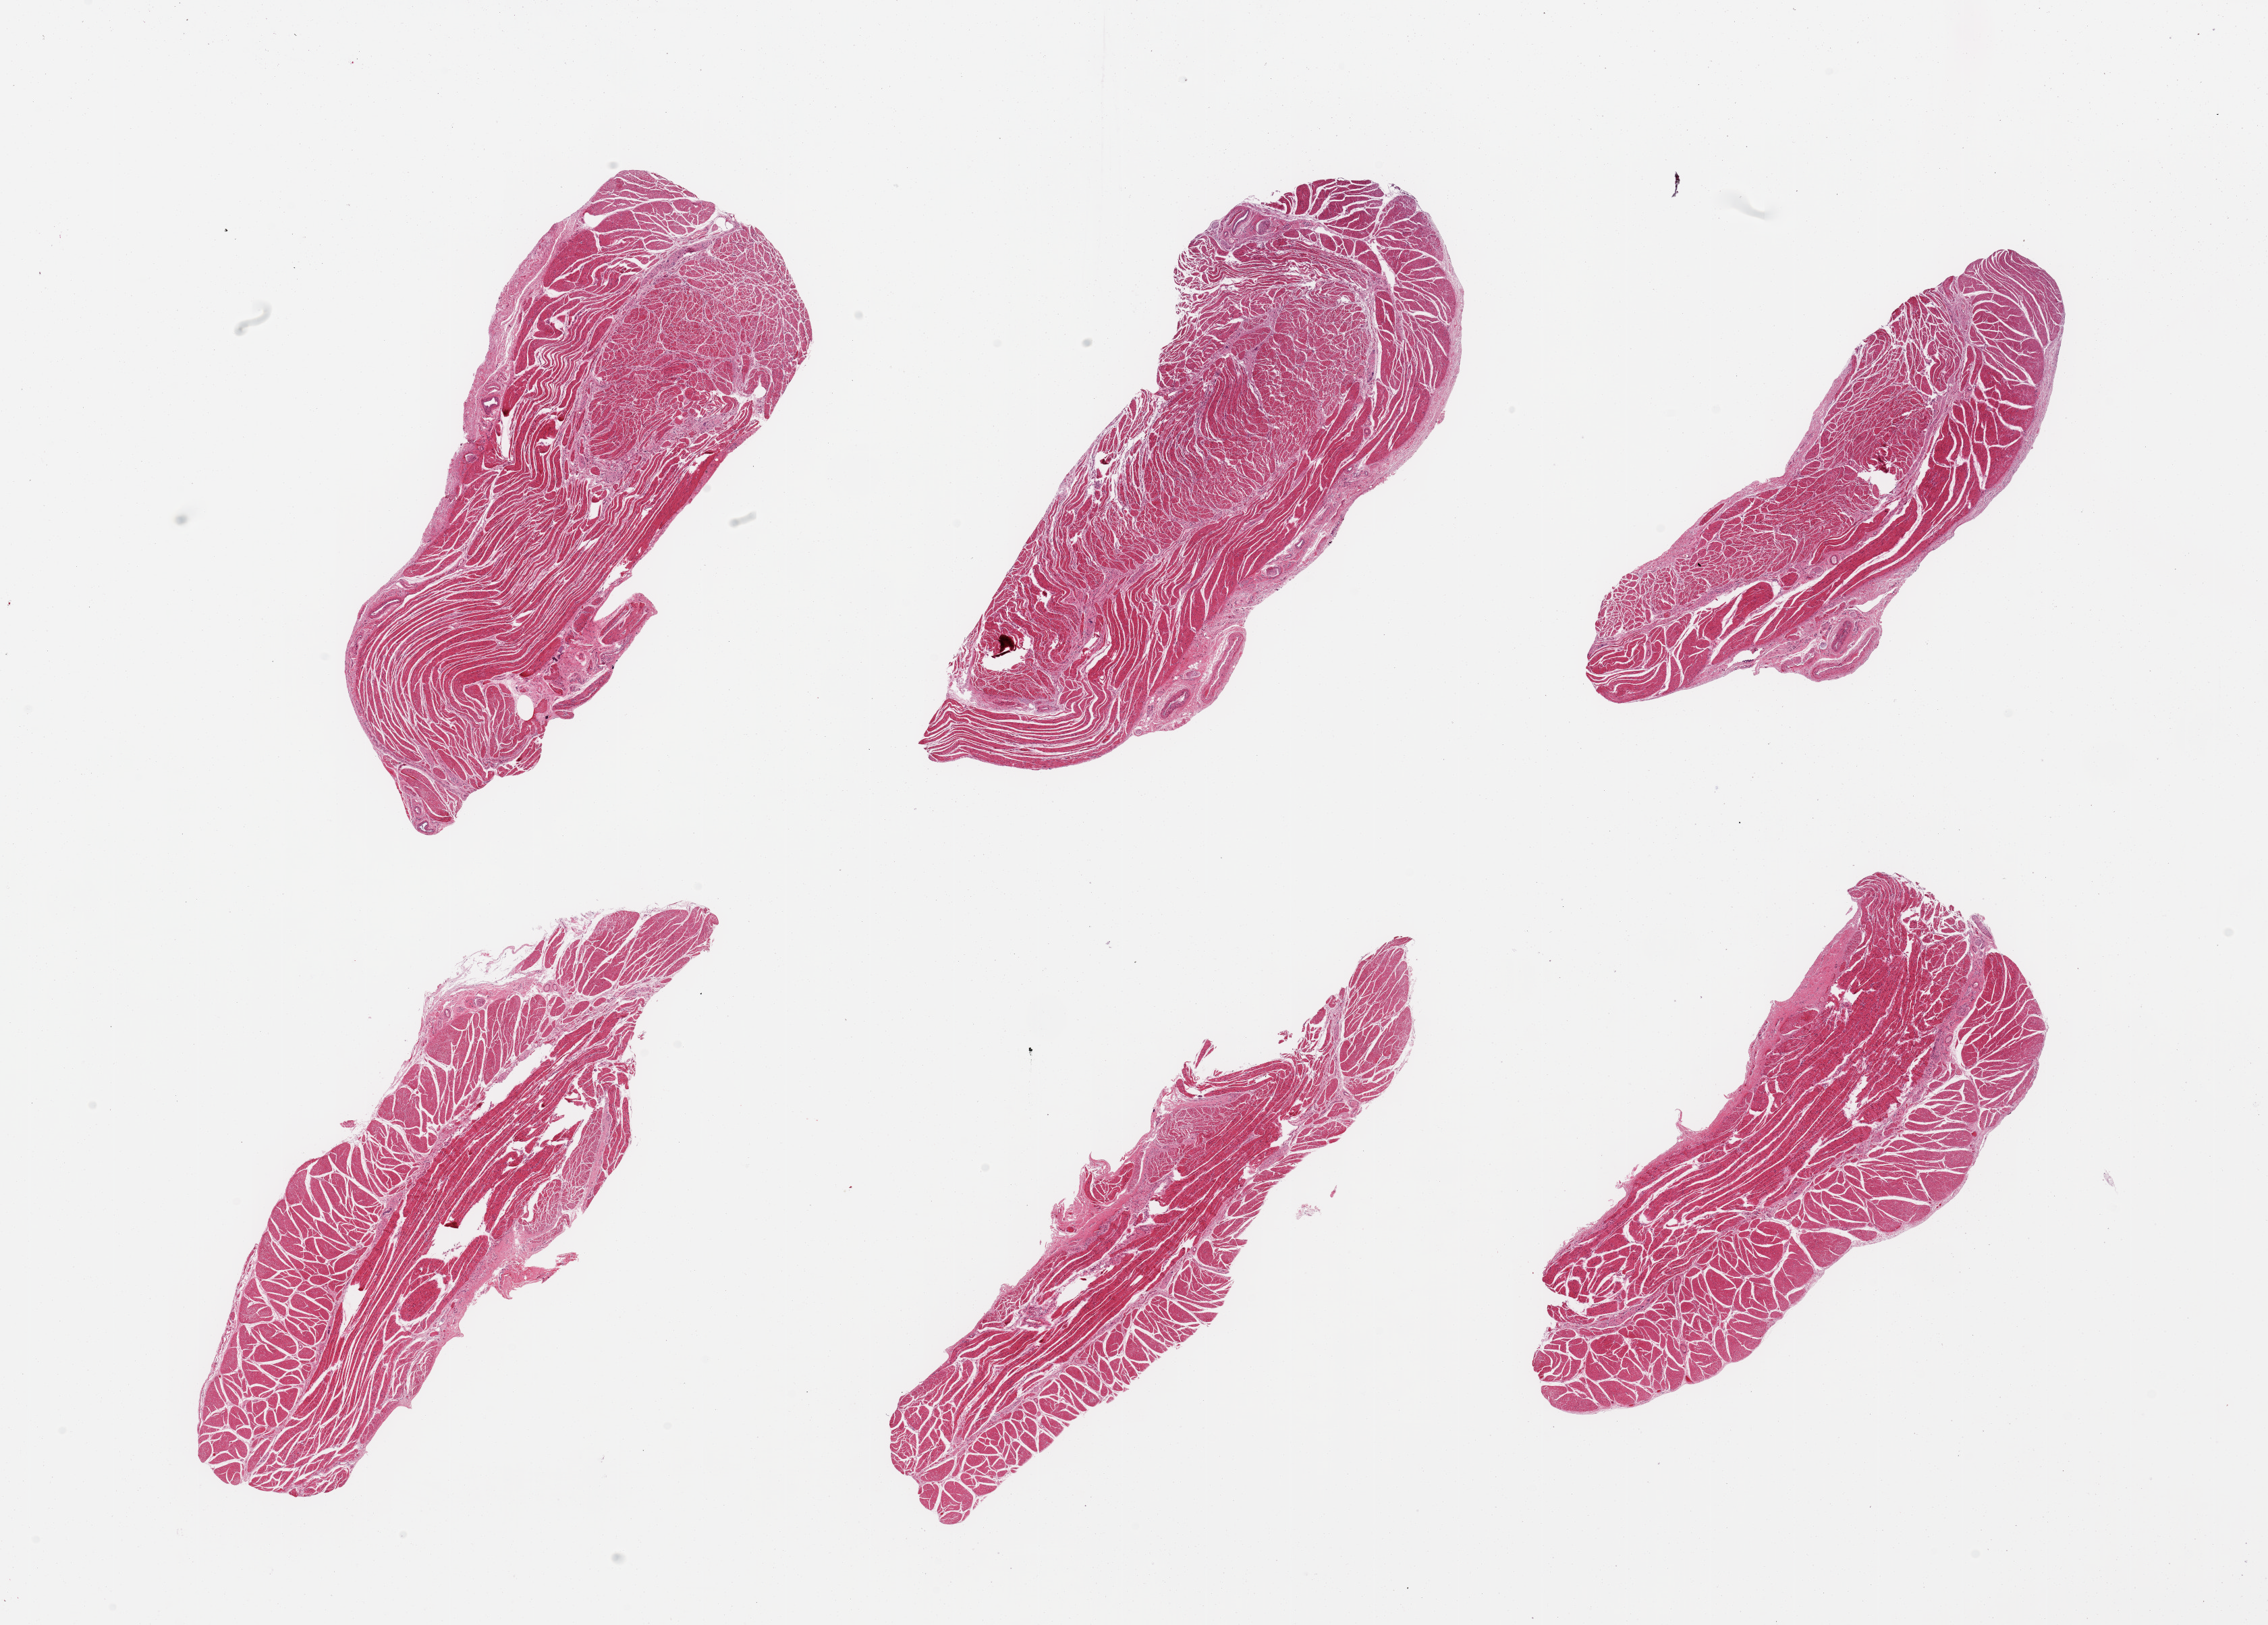
Digitized H&E-stained section, low-resolution overview of the scanned area, about 26.6 x 19.0 mm. PAXgene-fixed, paraffin-embedded tissue. Section of esophageal muscle (target tissue). Donor tissue sample.
Pathologist's review note for this sample: 6 pieces; well trimmed target muscularis.